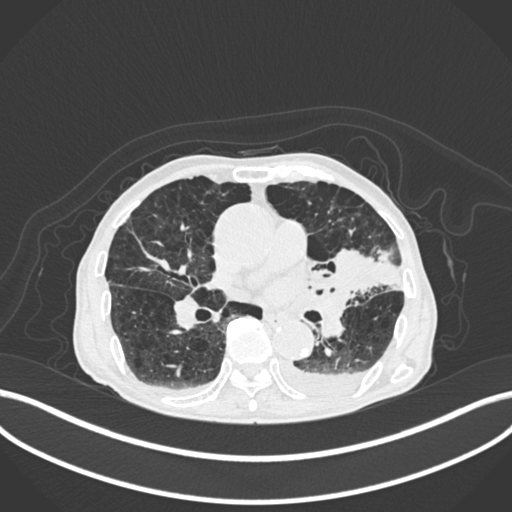
Chest CT, one axial slice. Slice 110 of 400 in the series (ordered by position). Reconstruction kernel B30f. 120 kVp. Lung window (W 1500 / L -600 HU). 512 × 512 image matrix, field of view 400 × 400 mm. Male patient, age 90 years or older. Case-level facts recorded for this patient, not image findings: clinical TNM (as recorded): T2b N1 M0.
Structures marked on this image (bounding box drawn by a radiologist):
- lung tumour (recorded histology: squamous cell carcinoma): box from (x=331, y=243) to (x=396, y=290) px